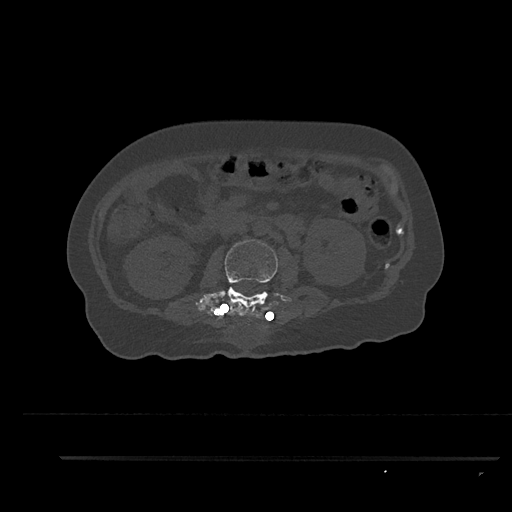
CT including the spine, one axial slice. Position 148 of 797 along the scan axis. 120 kVp. Bone window (W 1800 / L 400 HU). 0.5 mm slice thickness. 512 × 512 image matrix, field of view 408 × 408 mm. Patient: female, 44 years. Case-level facts recorded for this patient, not image findings: primary cancer: renal.
Structures marked on this image (semi-automatic segmentation, software-assisted and operator-edited):
- L2 vertebra: box from (x=195, y=239) to (x=280, y=326) px